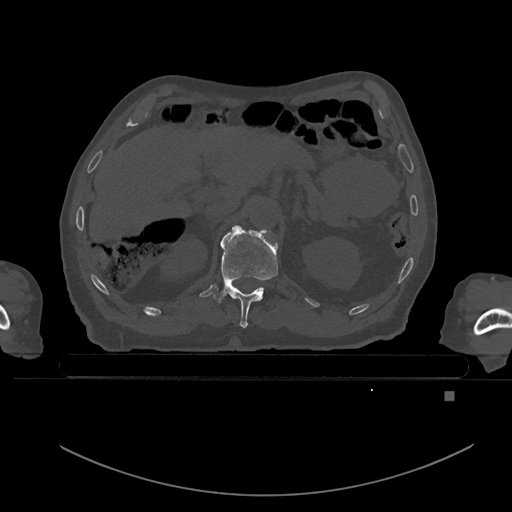
CT including the spine, one axial slice; position 16 of 969 along the scan axis; bone window (W 1800 / L 400 HU); 0.5 mm slice thickness; 512 × 512 image matrix. Male patient, age 82 years. Case-level facts recorded for this patient, not image findings: primary cancer: prostate; vertebrae with lytic lesions (as recorded): T11, T9, T8, T2.
Outlined on this slice (semi-automatic segmentation, software-assisted and operator-edited):
- T11 vertebra: bounding box (x1, y1, x2, y2) in pixels: (213, 227, 278, 328)